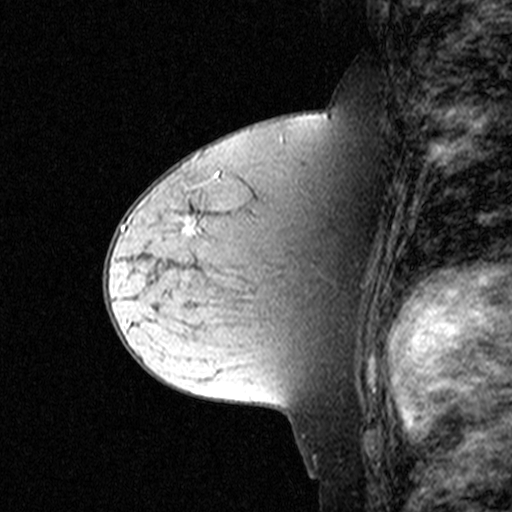
Breast MRI (dynamic contrast-enhanced), one sagittal slice. Position 24 of 44 along the scan axis. Dynamic contrast-enhanced study with each time point stored as its own series, time point 2 of 3 at this slice position (early post-contrast, ordered by acquisition time). 1.5 T. TE 4.5 ms, TR 11 ms. 3 mm slice thickness. 512 × 512 image matrix. Female patient, age 44 years. Case-level facts recorded for this patient, not image findings: setting: breast cancer imaged before/during neoadjuvant chemotherapy; receptor status: triple-negative.
Annotated regions visible in this slice (semi-automatic segmentation, software-assisted and operator-edited):
- analysis volume of interest (the breast-tissue region the enhancement analysis was run in; not a lesion): bounding box [x1, y1, x2, y2] px = [174, 204, 303, 305]
- tumour enhancement mask (voxels above the 90 % enhancement threshold inside the analysis volume of interest): [183, 215, 196, 235]